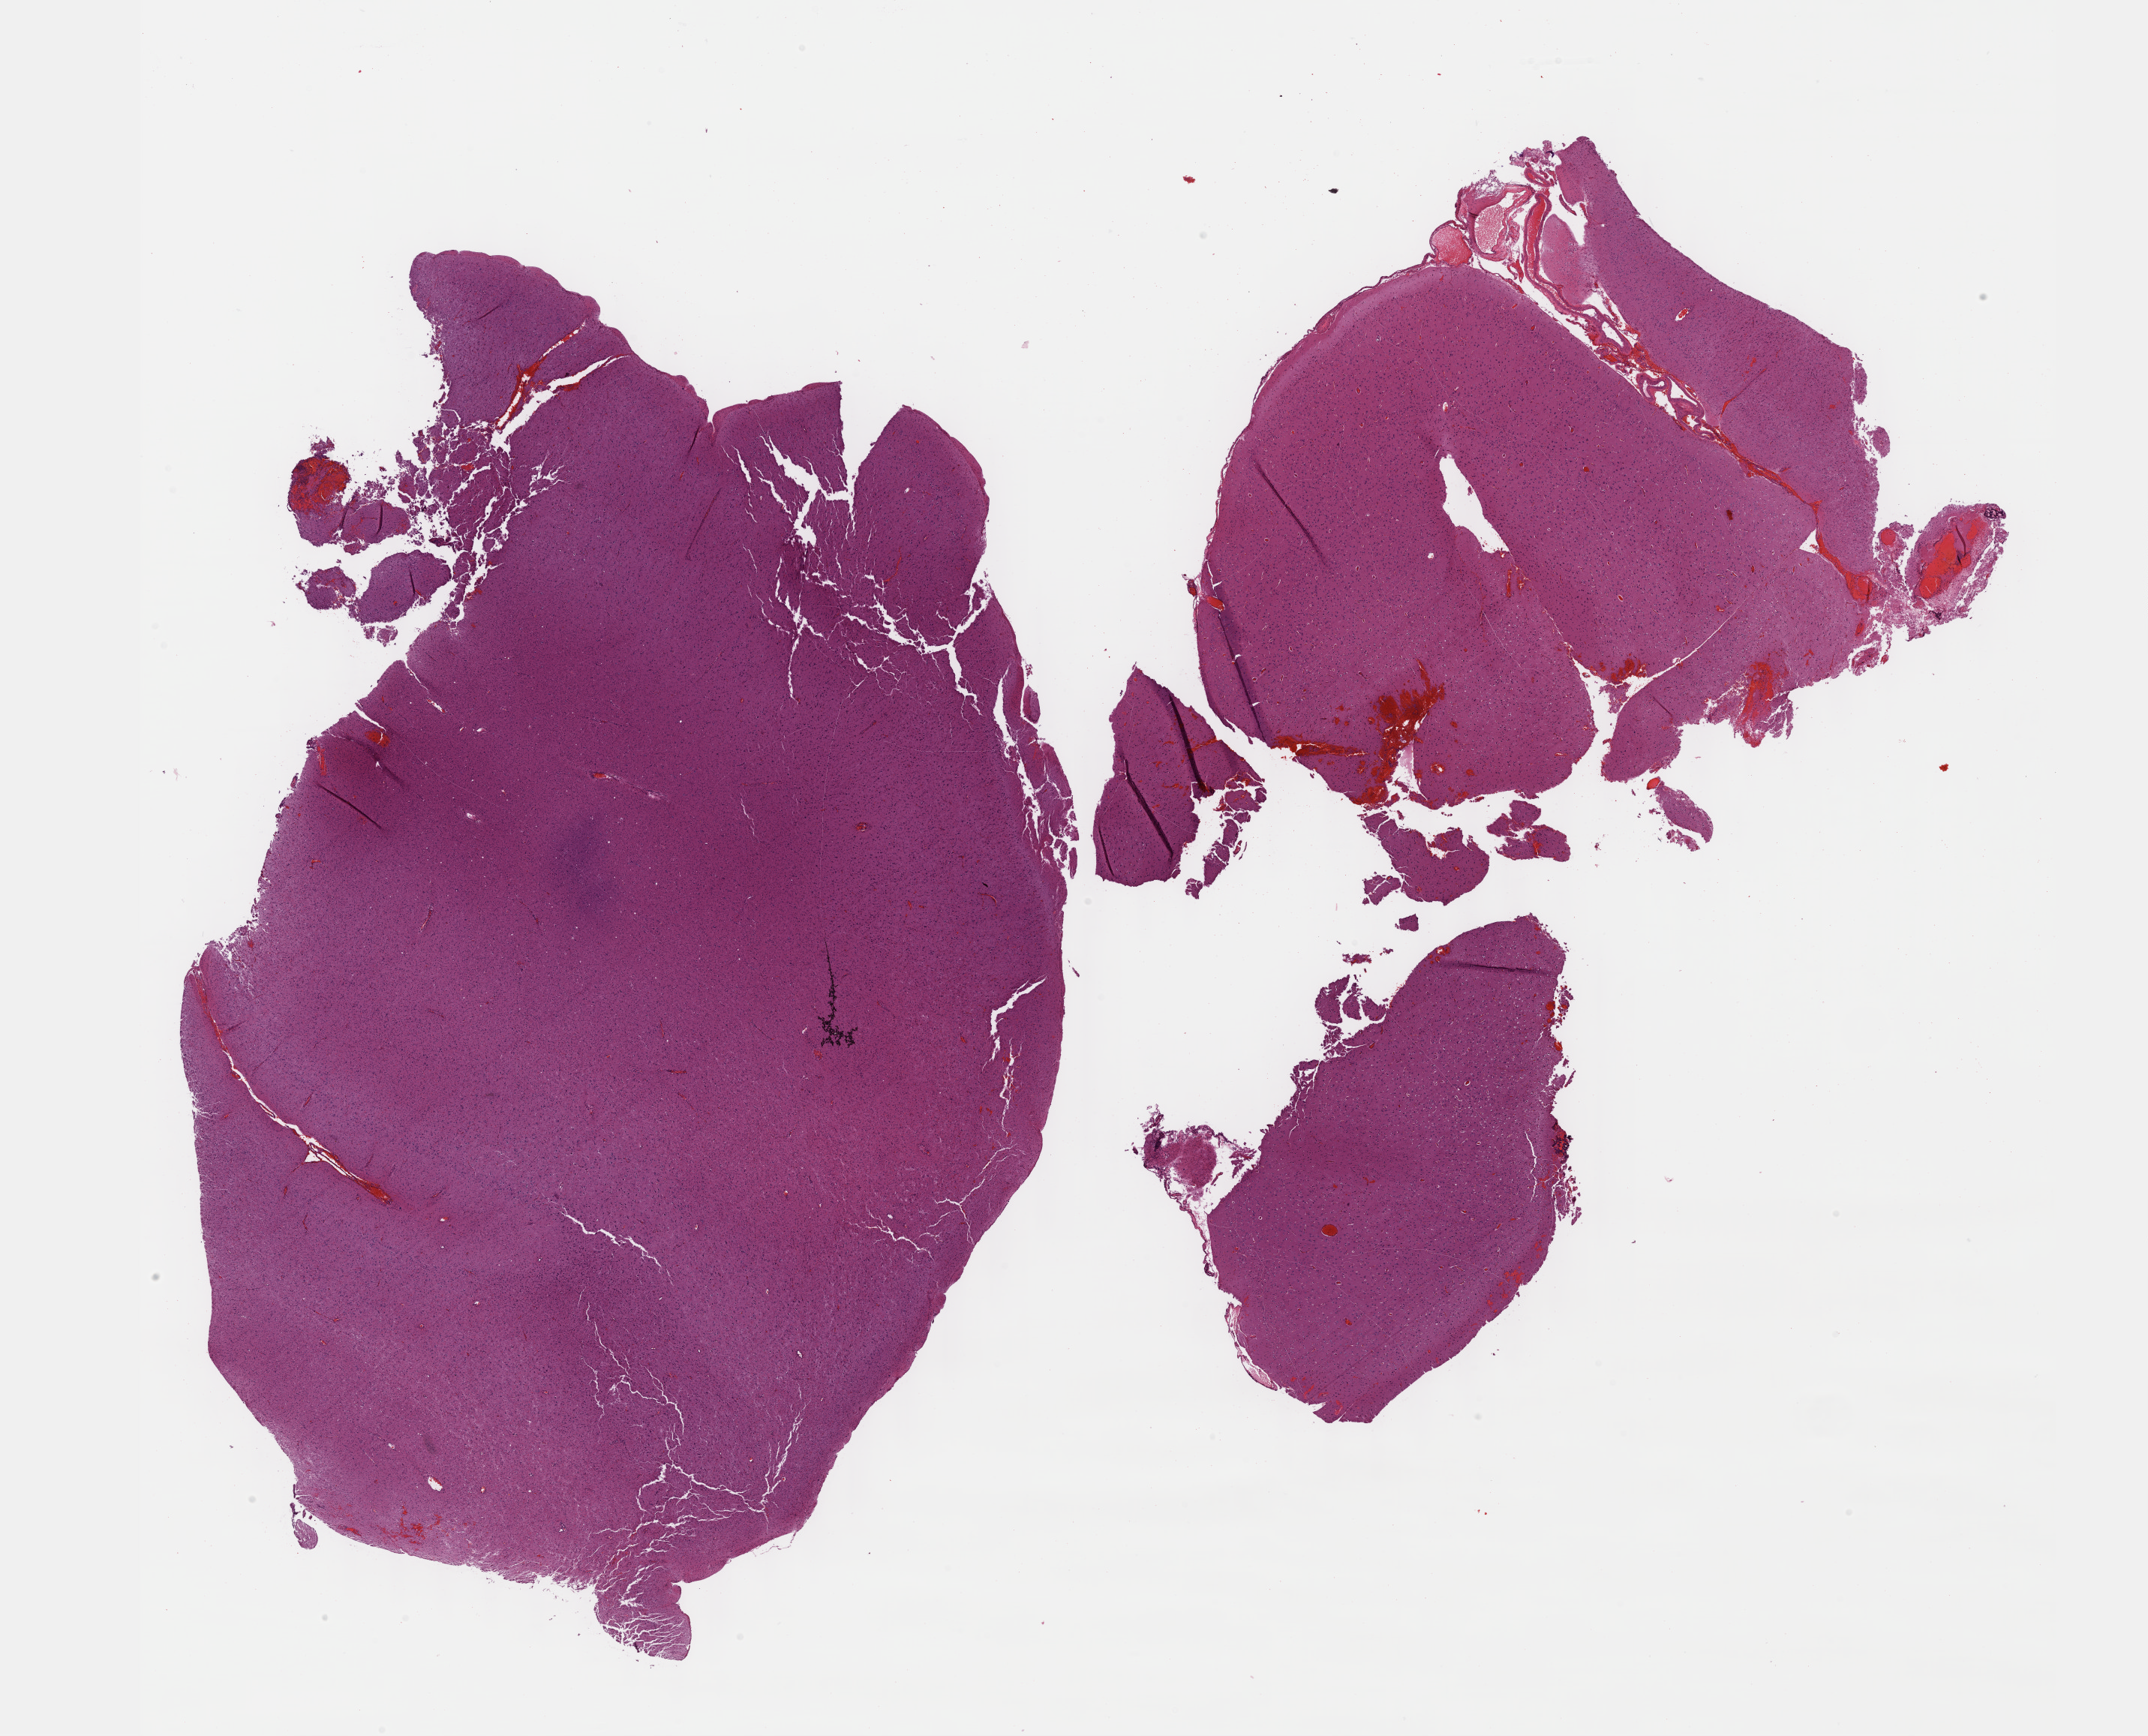
Digitized H&E tissue section (whole slide) — a low-resolution overview of the entire scanned area, about 23.1 x 18.7 mm (slide scanned at 40x). FFPE section. Sample: primary tumour, brain. Male patient; age at initial diagnosis 62 years.
Histologic diagnosis: Astrocytoma, NOS (cerebrum).